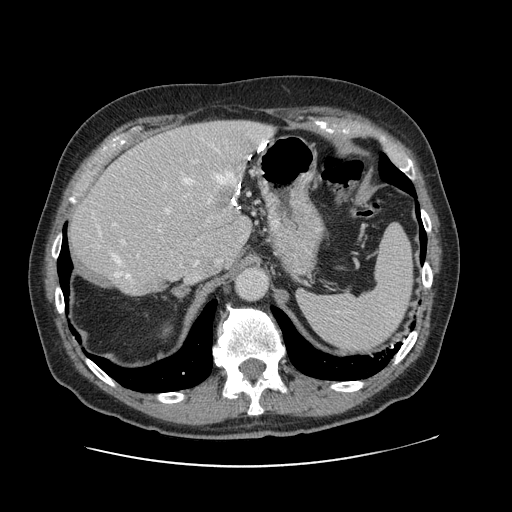
Contrast-enhanced abdominal CT, one axial slice. Position 83 of 138 along the scan axis. 120 kVp. Soft-tissue window (W 400 / L 40 HU). 2.5 mm slice thickness. 512 × 512 image matrix, field of view 402 × 402 mm. Male patient, age 71 years. From the clinical record (not read from this slice): diagnosis: colorectal cancer liver metastases, imaged before liver resection; multiple liver metastases: no; largest metastasis: 3.3 cm; disease in both lobes: no.
Structures marked on this image (expert manual segmentation):
- hepatic veins: bounding box [x1, y1, x2, y2] px = [98, 140, 267, 280]
- liver: [69, 122, 271, 294]
- planned liver remnant (the part of the liver to remain after resection): [69, 151, 239, 295]
- portal vein (with intrahepatic branches): [119, 161, 197, 245]
- liver metastasis: [212, 186, 236, 209]